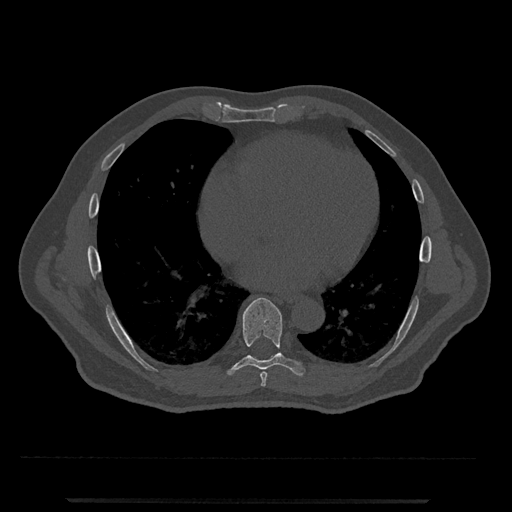
CT including the spine, one axial slice; position 630 of 797 along the scan axis; bone window (W 1800 / L 400 HU); 512 × 512 image matrix, field of view 419 × 419 mm. Patient: male, 63 years. From the clinical record (not read from this slice): primary cancer: prostate.
Outlined on this slice (semi-automatic segmentation, software-assisted and operator-edited):
- T7 vertebra: bounding box [x1, y1, x2, y2] px = [260, 372, 268, 387]
- T8 vertebra: [226, 298, 306, 376]